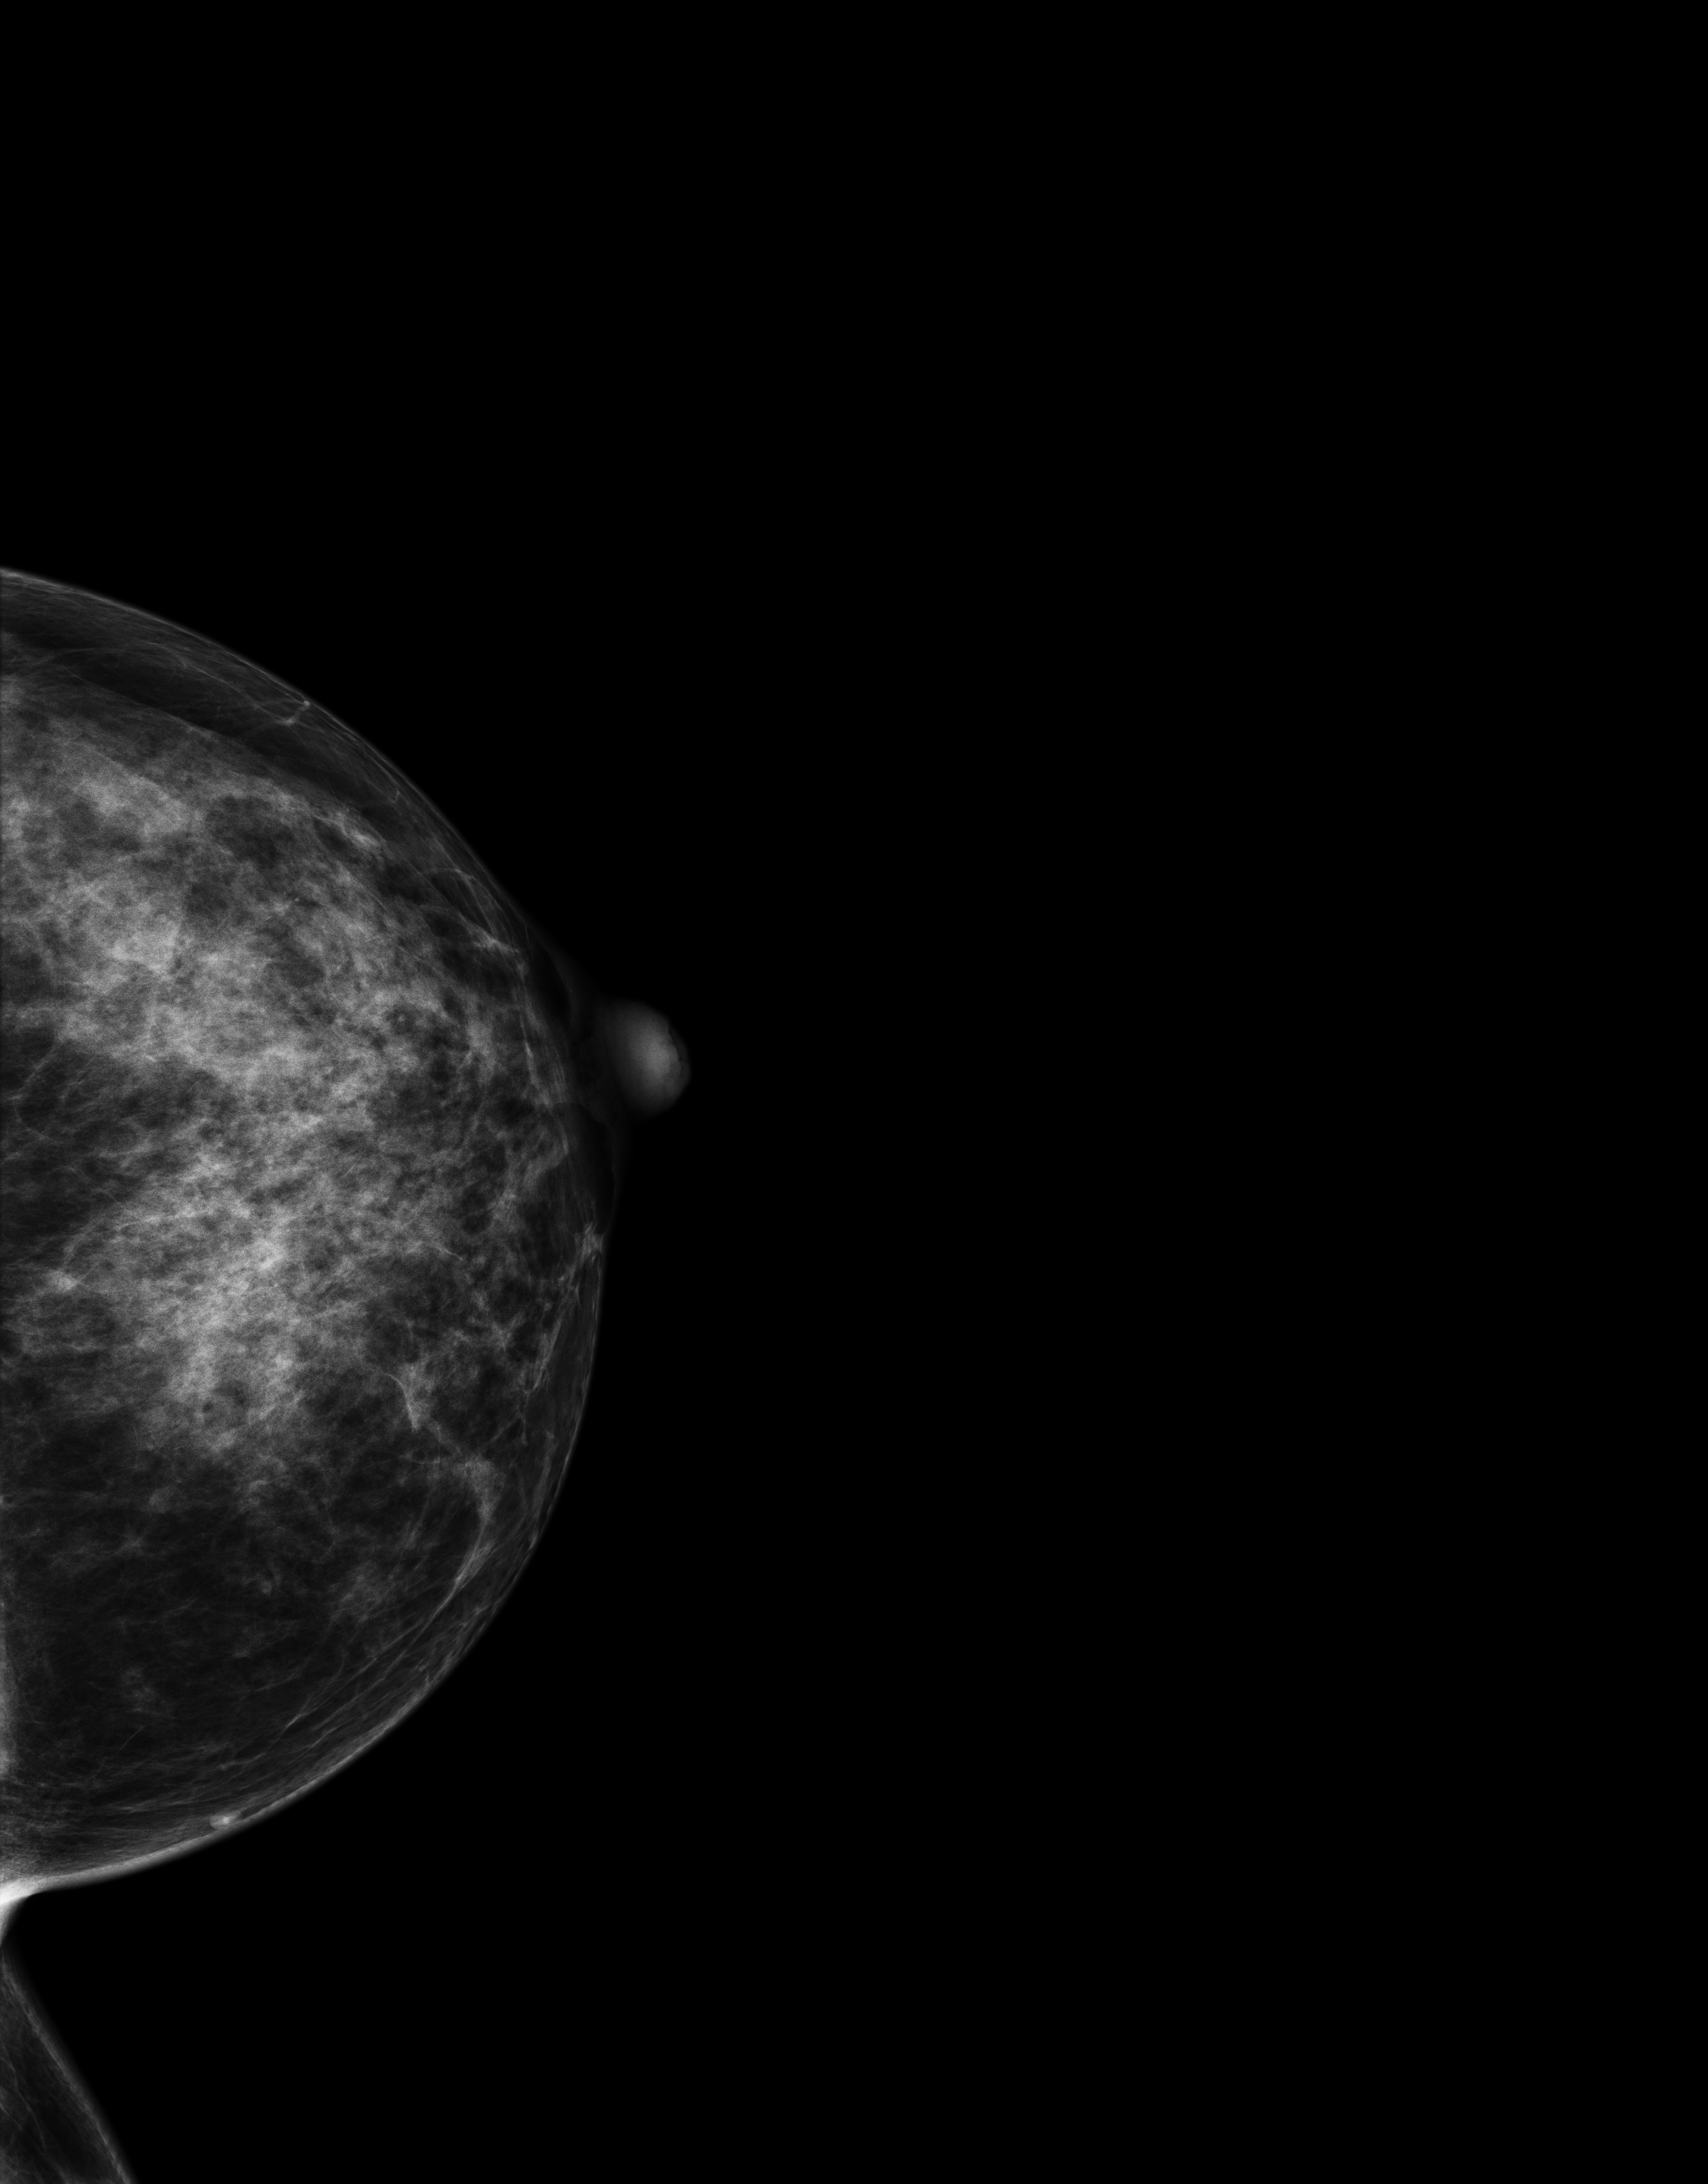
Digital mammogram (FFDM), left breast, cranio-caudal projection, screening examination, system: Senographe Essential ADS_56.21.3. Patient: female, 42 years.
BI-RADS breast density category at the screening exam (both breasts, scale 1–4): 4. Final BI-RADS category for the screening round (tomosynthesis exam, both breasts): category 1. Recall: no recall after this screen.